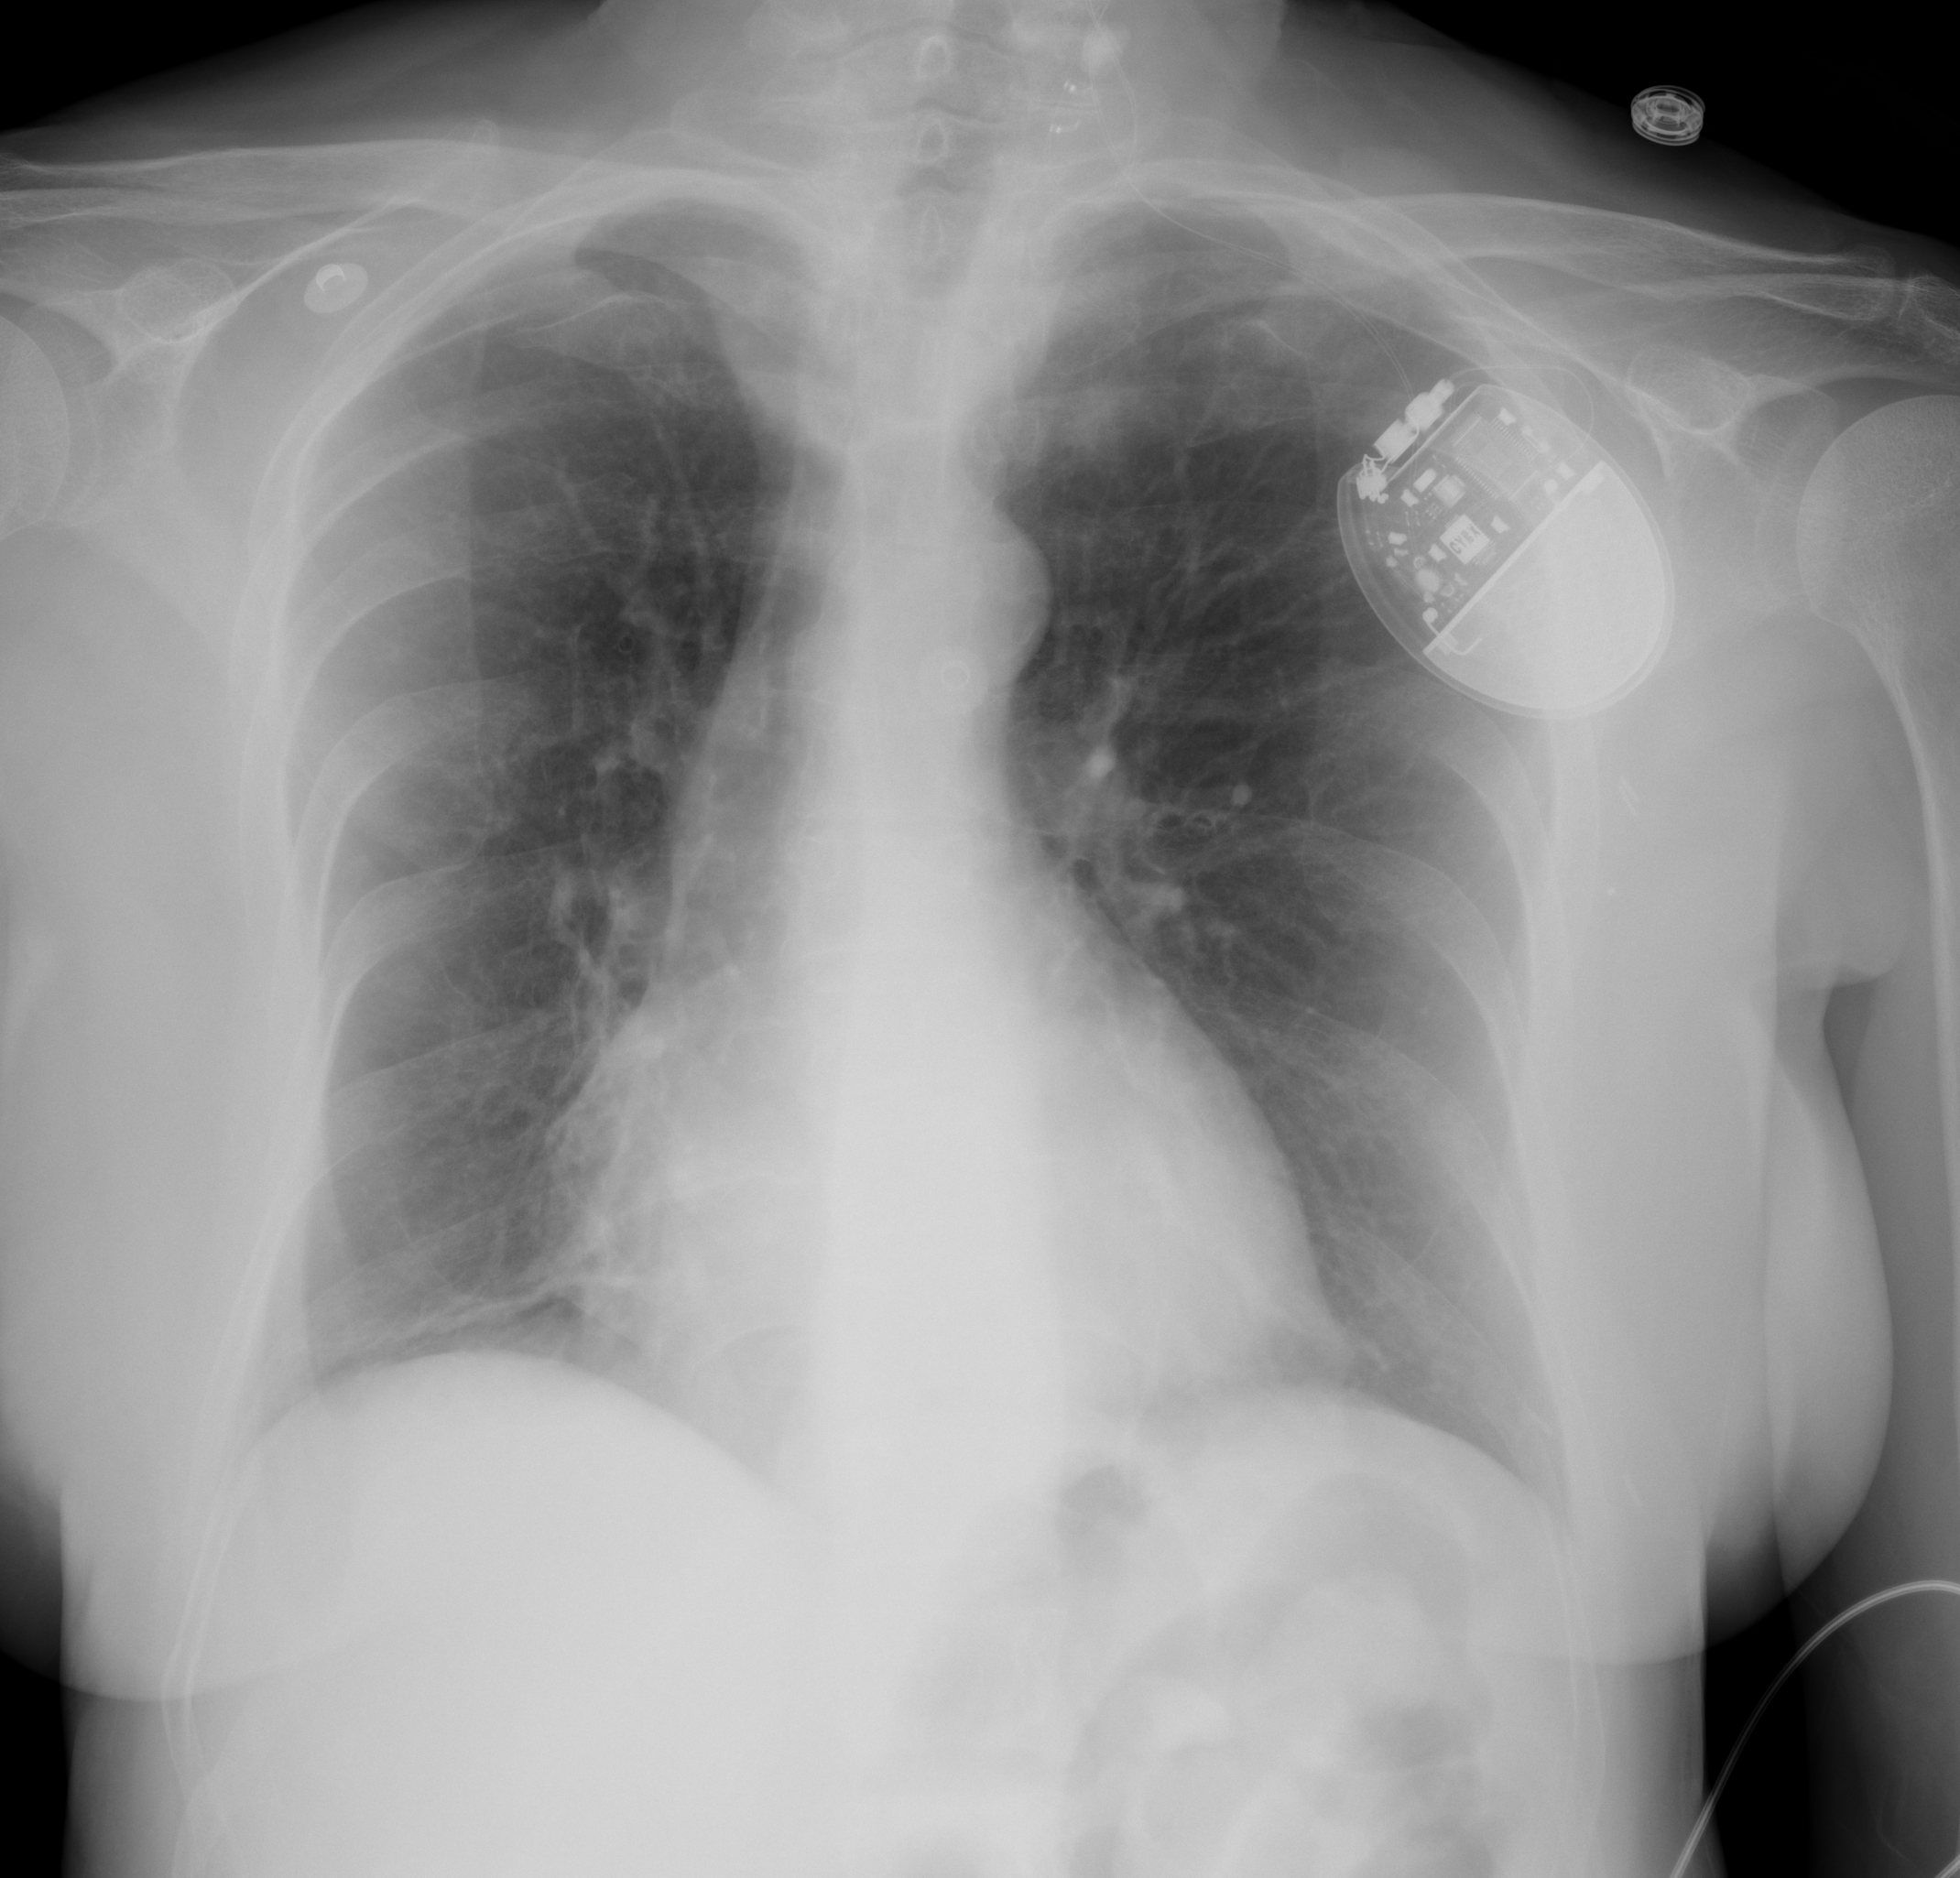
Portable chest radiograph, AP projection. Female patient, age 70 years; imaged 1 day before the COVID-19 diagnosis.
Radiologist's key findings for this exam: No significant airspace consolidation bilaterally.